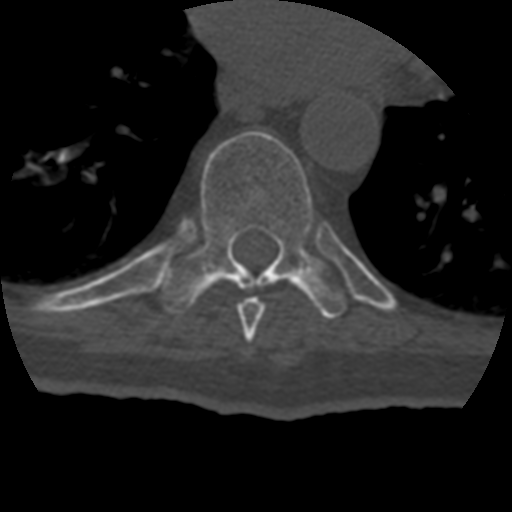
CT including the spine, one axial slice. Slice 246 of 399 in the series (ordered by position). Reconstruction kernel STANDARD. 120 kVp. Bone window (W 1800 / L 400 HU). 512 × 512 image matrix. Patient age 69 years. From the clinical record (not read from this slice): primary cancer: prostate.
Annotated regions visible in this slice (semi-automatically segmented with operator editing):
- T8 vertebra: bounding box <237,297,265,342> (left, top, right, bottom; pixels)
- T9 vertebra: <161,131,348,319>